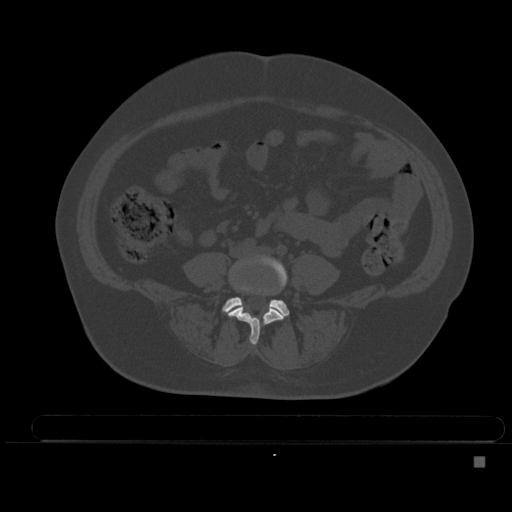
CT including the spine, one axial slice; bone window (W 1800 / L 400 HU); 1.5 mm slice thickness; 512 × 512 image matrix, field of view 404 × 404 mm. Female patient, age 33 years. Case-level facts recorded for this patient, not image findings: primary cancer: breast.
Annotated regions visible in this slice (semi-automatic segmentation, software-assisted and operator-edited):
- L4 vertebra: bounding box <228,255,288,345> (left, top, right, bottom; pixels)
- L5 vertebra: <223,297,289,317>